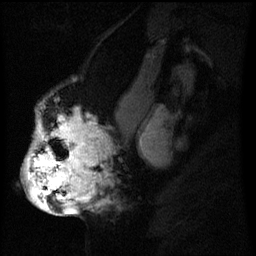
Breast MRI (dynamic contrast-enhanced), one sagittal slice; slice 31 of 60 in the series (ordered by position); dynamic contrast-enhanced series, image 2 of 3 at this slice position (ordered by acquisition); 1.5 T; TE 4.2 ms, TR 8 ms; 256 × 256 image matrix, field of view 200 × 200 mm. Female patient, age 50 years.
Structures marked on this image (semi-automatically segmented with operator editing):
- analysis volume of interest (the breast-tissue region the enhancement analysis was run in; not a lesion): box from (x=25, y=112) to (x=111, y=211) px
- tumour enhancement mask (voxels above the 70 % enhancement threshold inside the analysis volume of interest): (x=26, y=120)–(x=95, y=211)